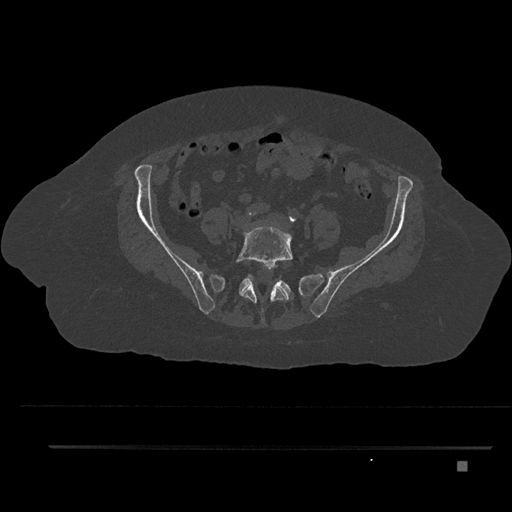
CT including the spine, one axial slice. Bone window (W 1800 / L 400 HU). 512 × 512 image matrix, field of view 437 × 437 mm. Female patient, age 76 years. Case-level facts recorded for this patient, not image findings: primary cancer: lung; vertebrae with lytic lesions (as recorded): T11, L3.
Outlined on this slice (semi-automatically segmented with operator editing):
- L5 vertebra: bounding box (x1, y1, x2, y2) in pixels: (235, 224, 293, 323)